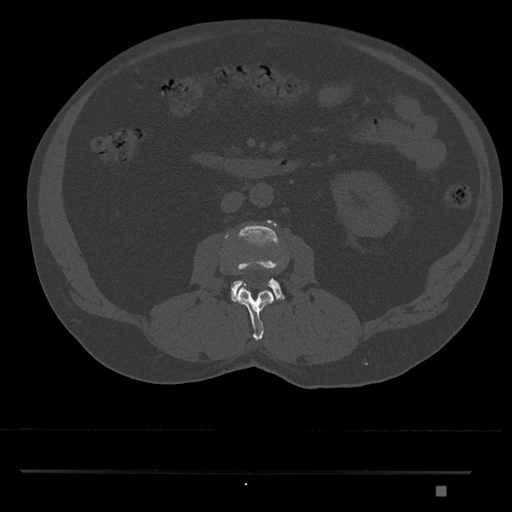
CT including the spine, one axial slice. Position 720 of 1134 along the scan axis. Reconstruction kernel Br40s/3. Bone window (W 1800 / L 400 HU). 0.5 mm slice thickness. 512 × 512 image matrix. Patient: male, 65 years. Case-level facts recorded for this patient, not image findings: primary cancer: prostate.
Structures marked on this image (semi-automatically segmented with operator editing):
- L2 vertebra: bounding box [x1, y1, x2, y2] px = [236, 286, 274, 341]
- L3 vertebra: [231, 220, 285, 303]